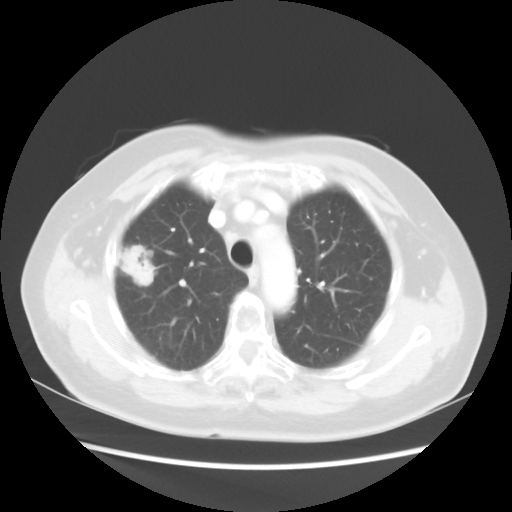
Chest CT, one axial slice. Position 36 of 48 along the scan axis. 100 kVp. Lung window (W 1500 / L -600 HU). 5 mm slice thickness. 512 × 512 image matrix, field of view 360 × 360 mm. Patient: female, 75 years. Case-level facts recorded for this patient, not image findings: clinical TNM (as recorded): T1c N0 M0.
Structures marked on this image (bounding box drawn by a radiologist):
- lung tumour (recorded histology: adenocarcinoma): bounding box [x1, y1, x2, y2] px = [112, 238, 160, 295]